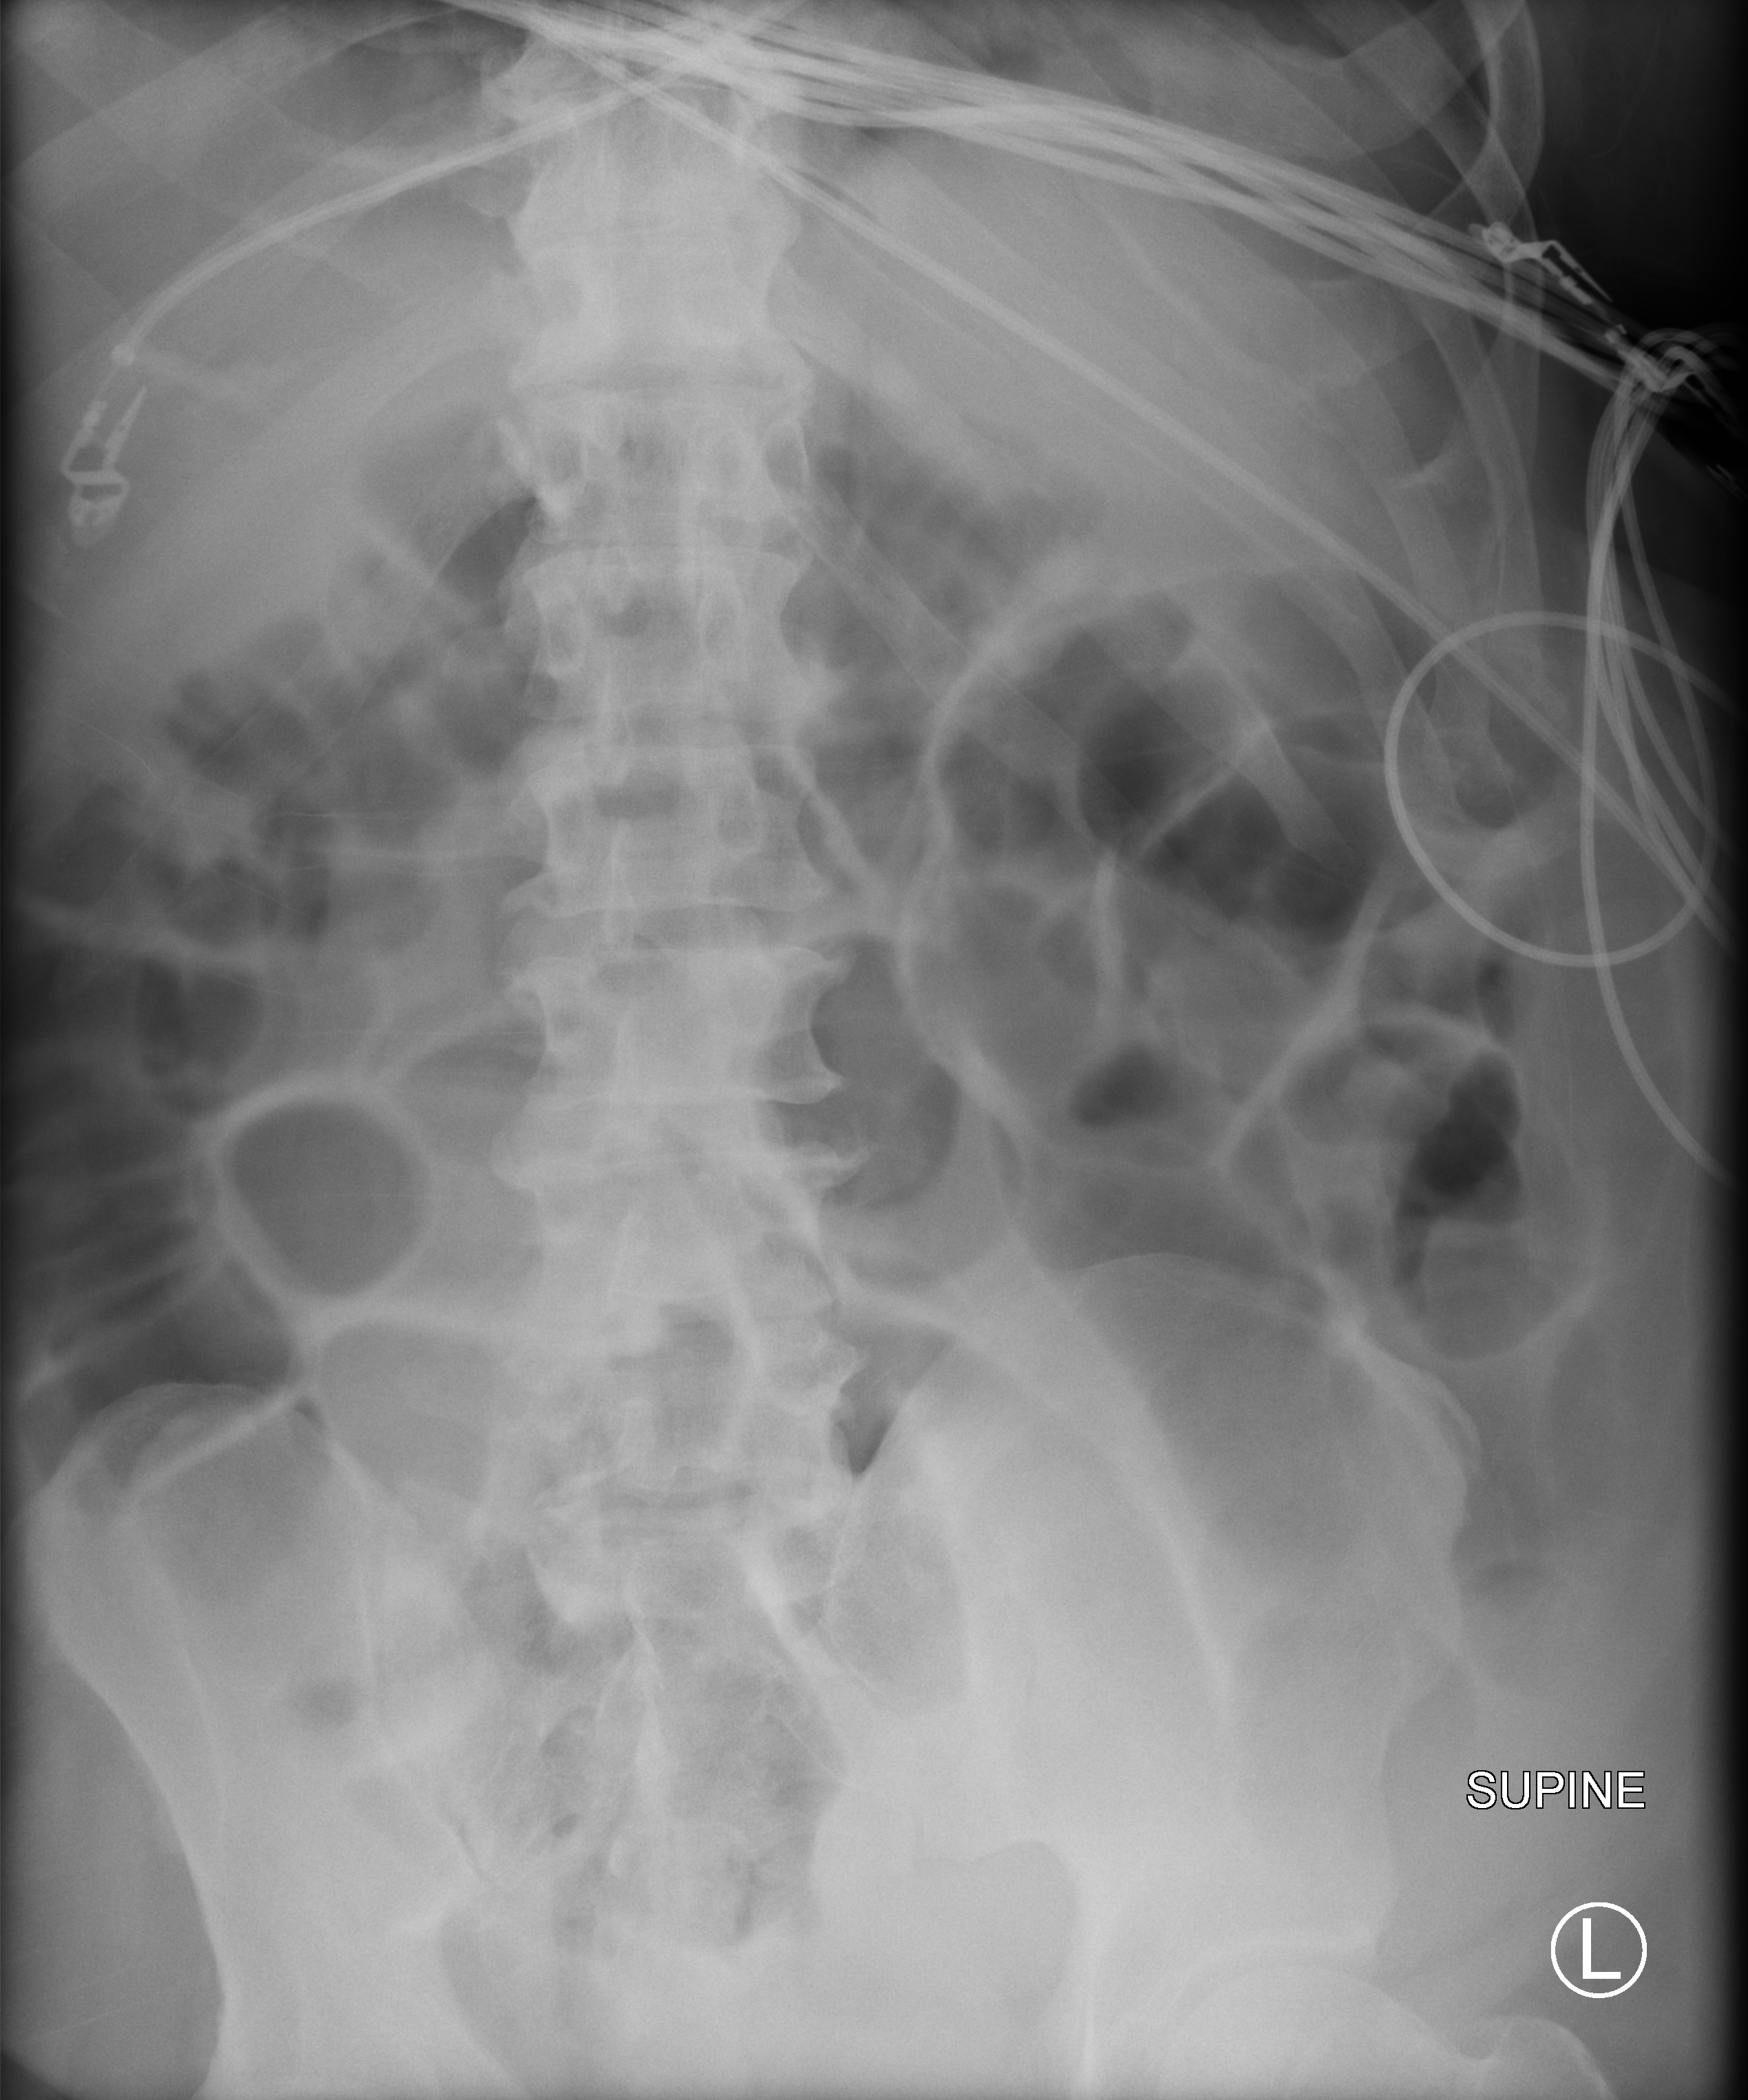
Bedside abdomen radiograph (computed radiography), anteroposterior (AP) projection. Male patient hospitalised with COVID-19, age 18–59 years.
Admission-level facts for this patient (not findings on this image; timing relative to this image not recorded): admitted to intensive care during this hospital stay: yes.